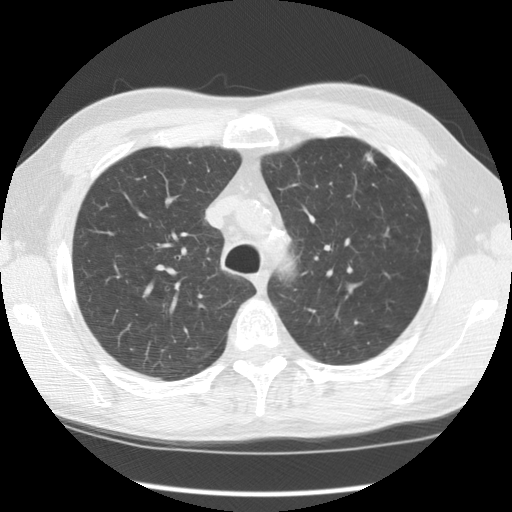
Low-dose screening chest CT, one axial slice. Reconstruction kernel STANDARD. 120 kVp. Lung window (W 1500 / L -600 HU). 2.5 mm slice thickness. 512 × 512 image matrix, field of view 350 × 350 mm.
Outlined on this slice (manually delineated by an expert):
- lesion 1 (tumor, upper lobe of left lung): bounding box <365,153,373,162> (left, top, right, bottom; pixels)